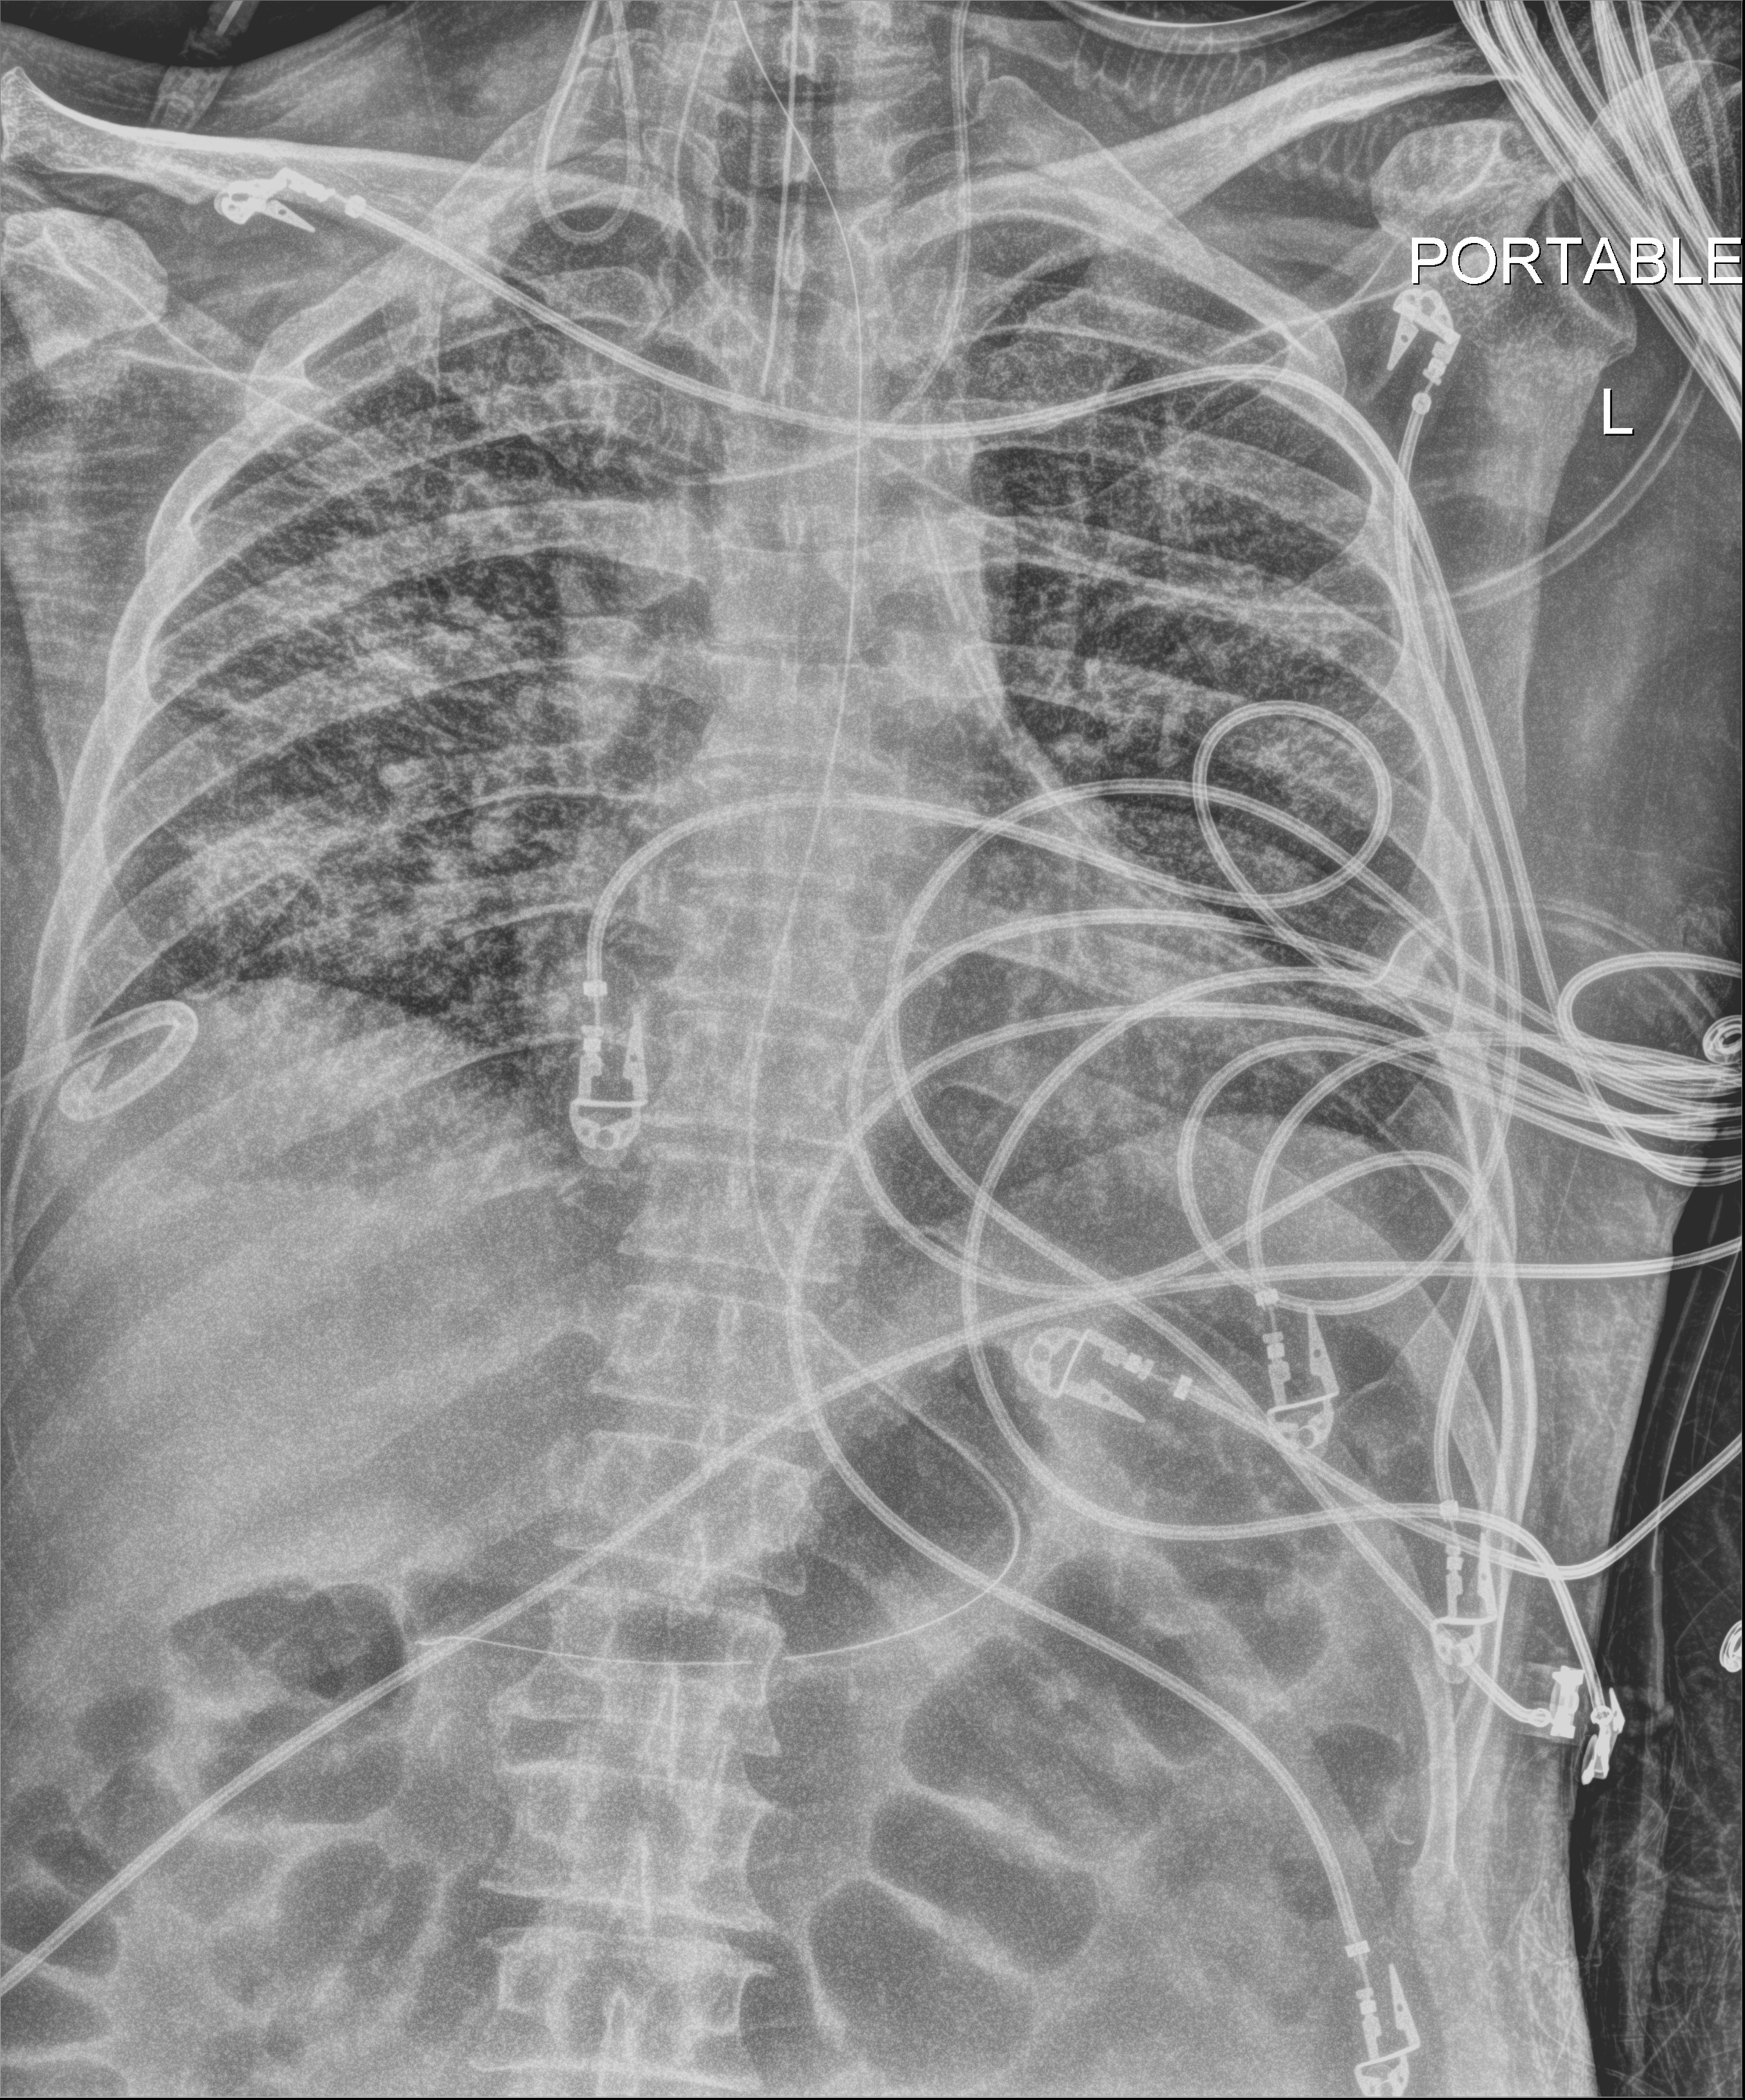
Bedside chest radiograph (digital radiography); anteroposterior (AP) projection. Male patient hospitalised with COVID-19, age 18–59 years.
From the hospital-stay record, not from the radiograph (when in the stay this image was taken is not recorded): mechanically ventilated during this hospital stay: yes; hypertension (admission record): no.